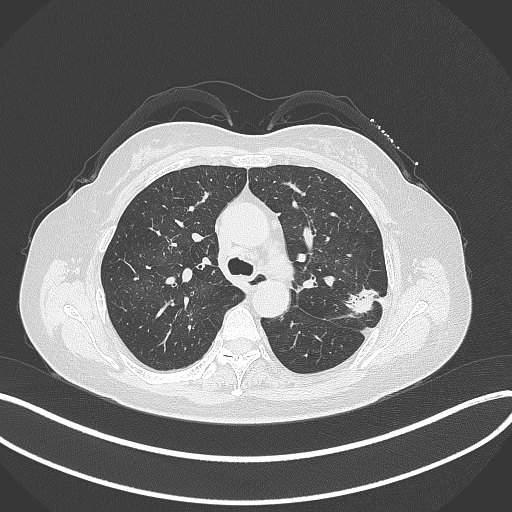
Chest CT, one axial slice. Position 218 of 319 along the scan axis. Reconstruction kernel B70f. Lung window (W 1500 / L -600 HU). 1 mm slice thickness. 512 × 512 image matrix, field of view 400 × 400 mm. Patient: female, 60 years. From the clinical record (not read from this slice): clinical TNM (as recorded): T1c N0 M0.
Structures marked on this image (rectangle marked by the reading radiologist):
- lung tumour (recorded histology: adenocarcinoma): box from (x=340, y=283) to (x=376, y=318) px